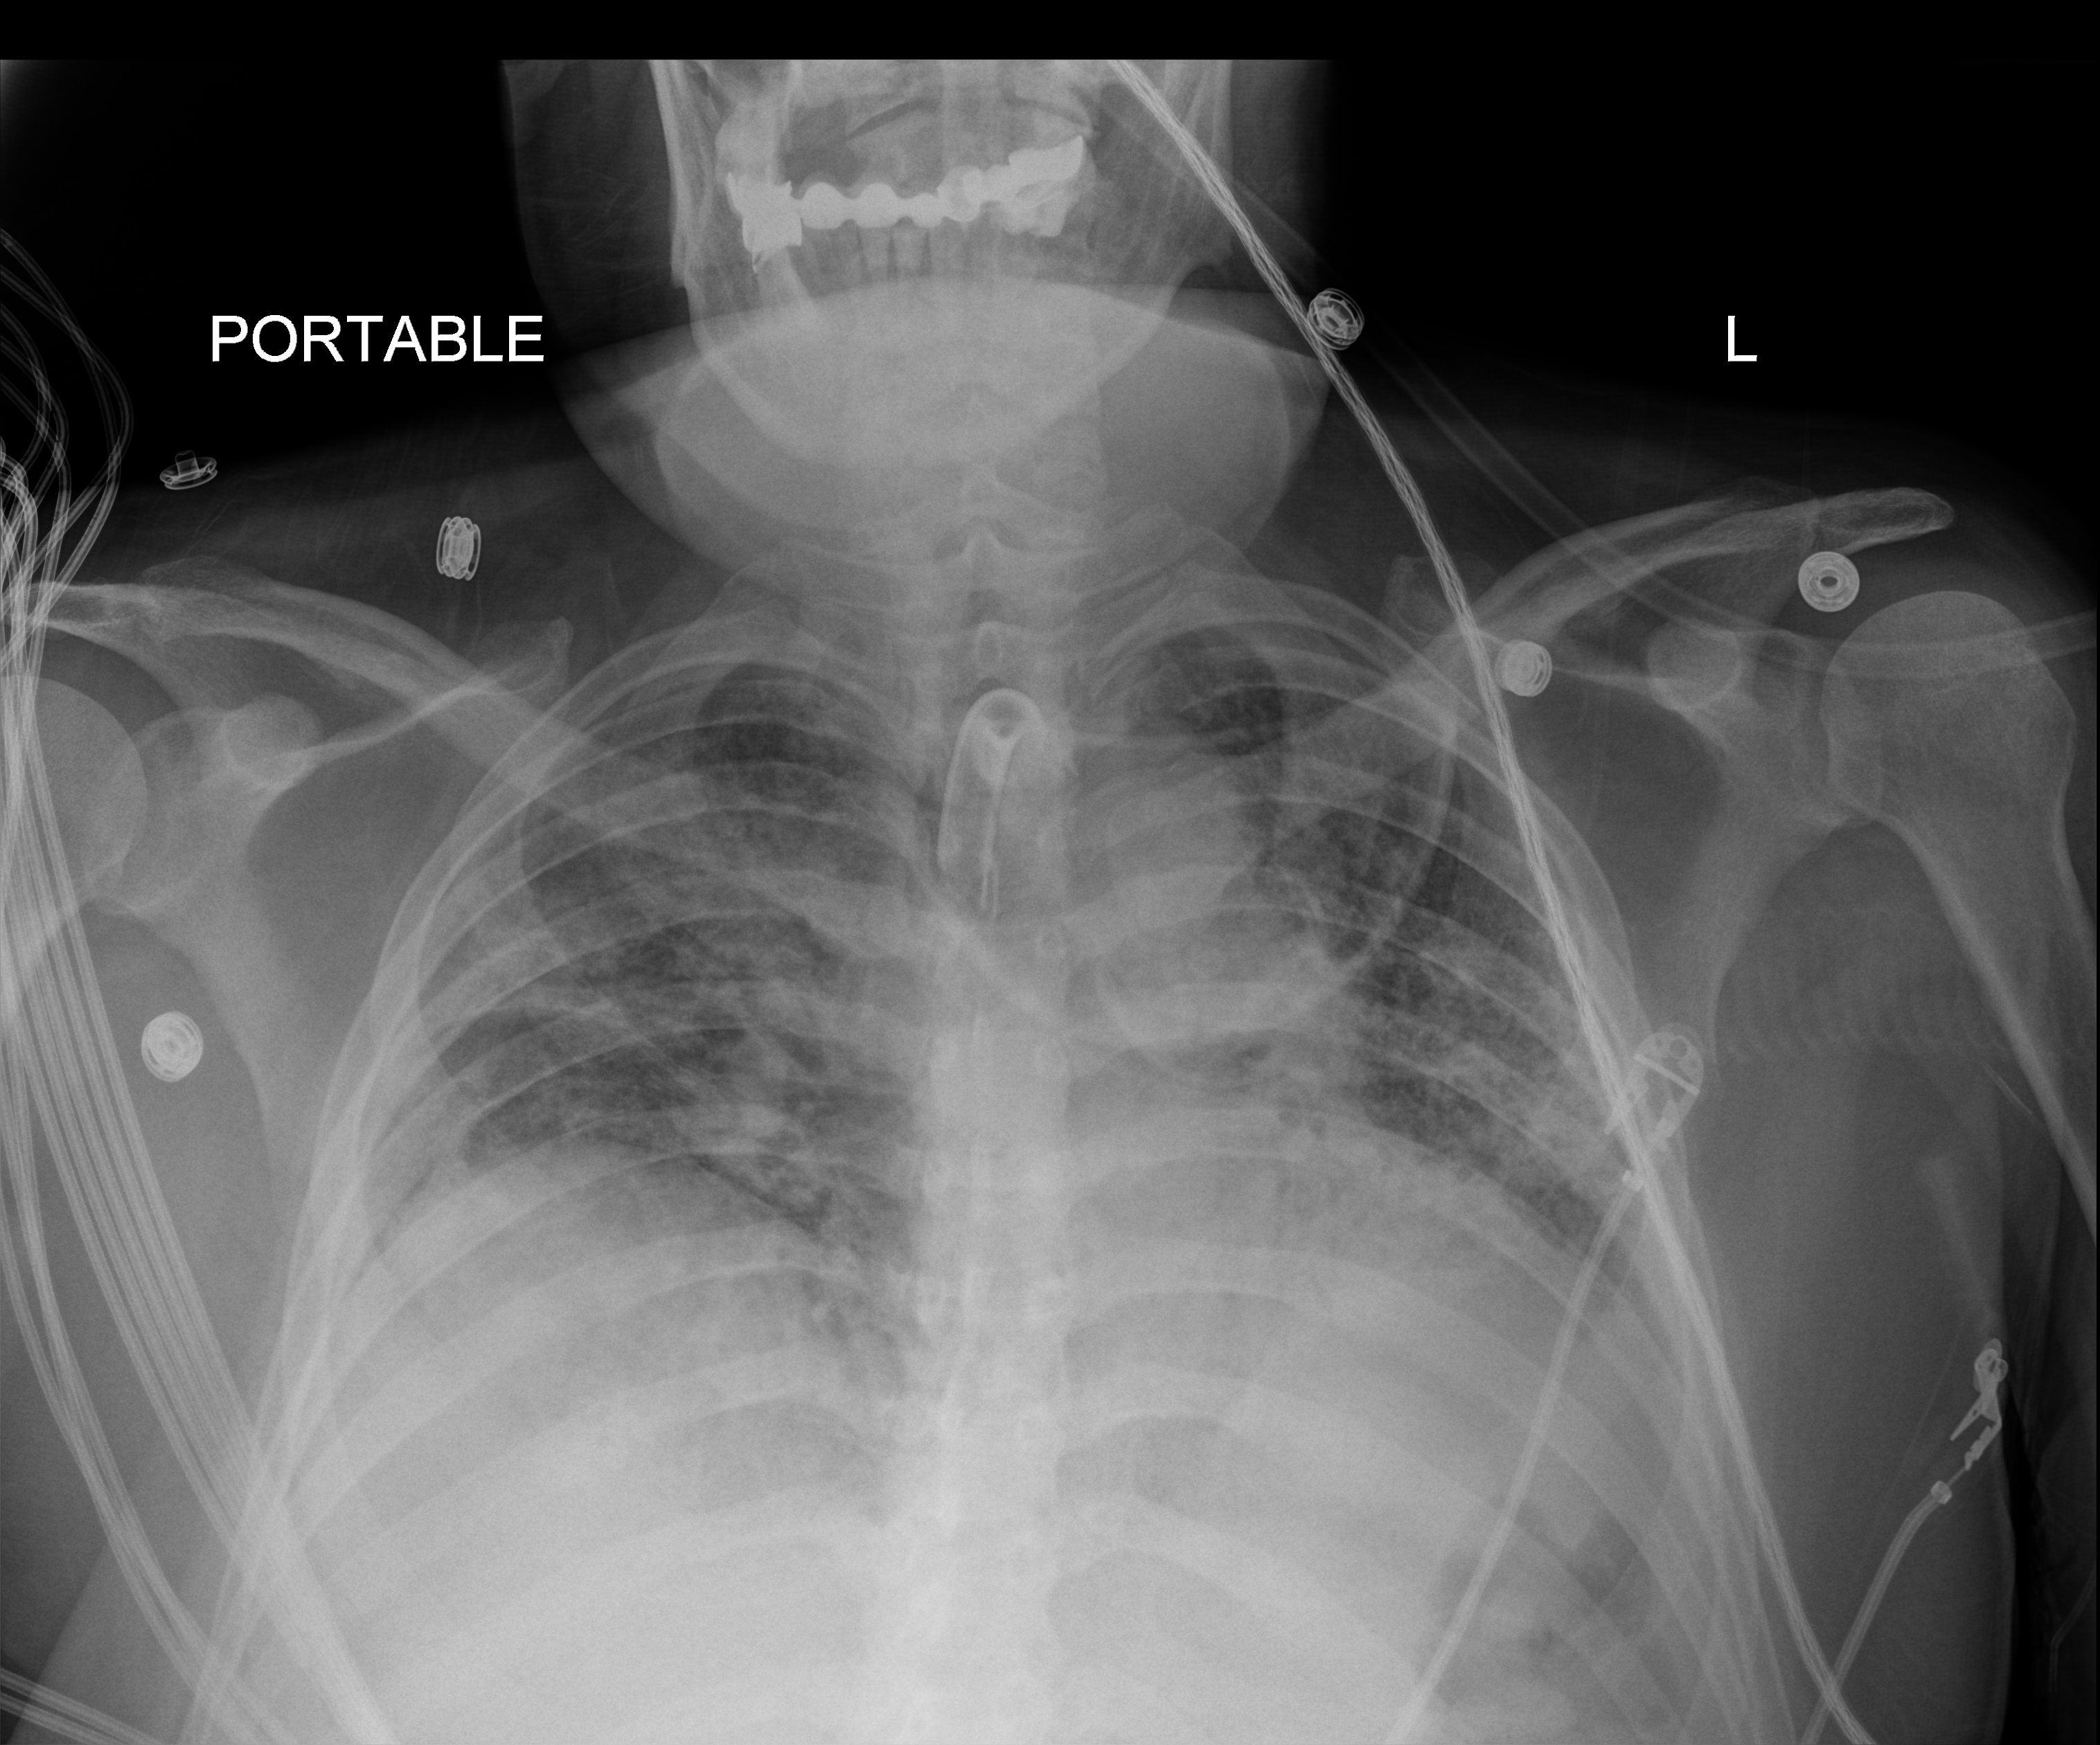
Portable chest radiograph, anteroposterior (AP) projection. Male patient hospitalised with COVID-19, age 18–59 years.
From the hospital-stay record, not from the radiograph (when in the stay this image was taken is not recorded):
- other chronic lung disease (admission record): no
- admitted to intensive care during this hospital stay: yes
- COPD (admission record): no